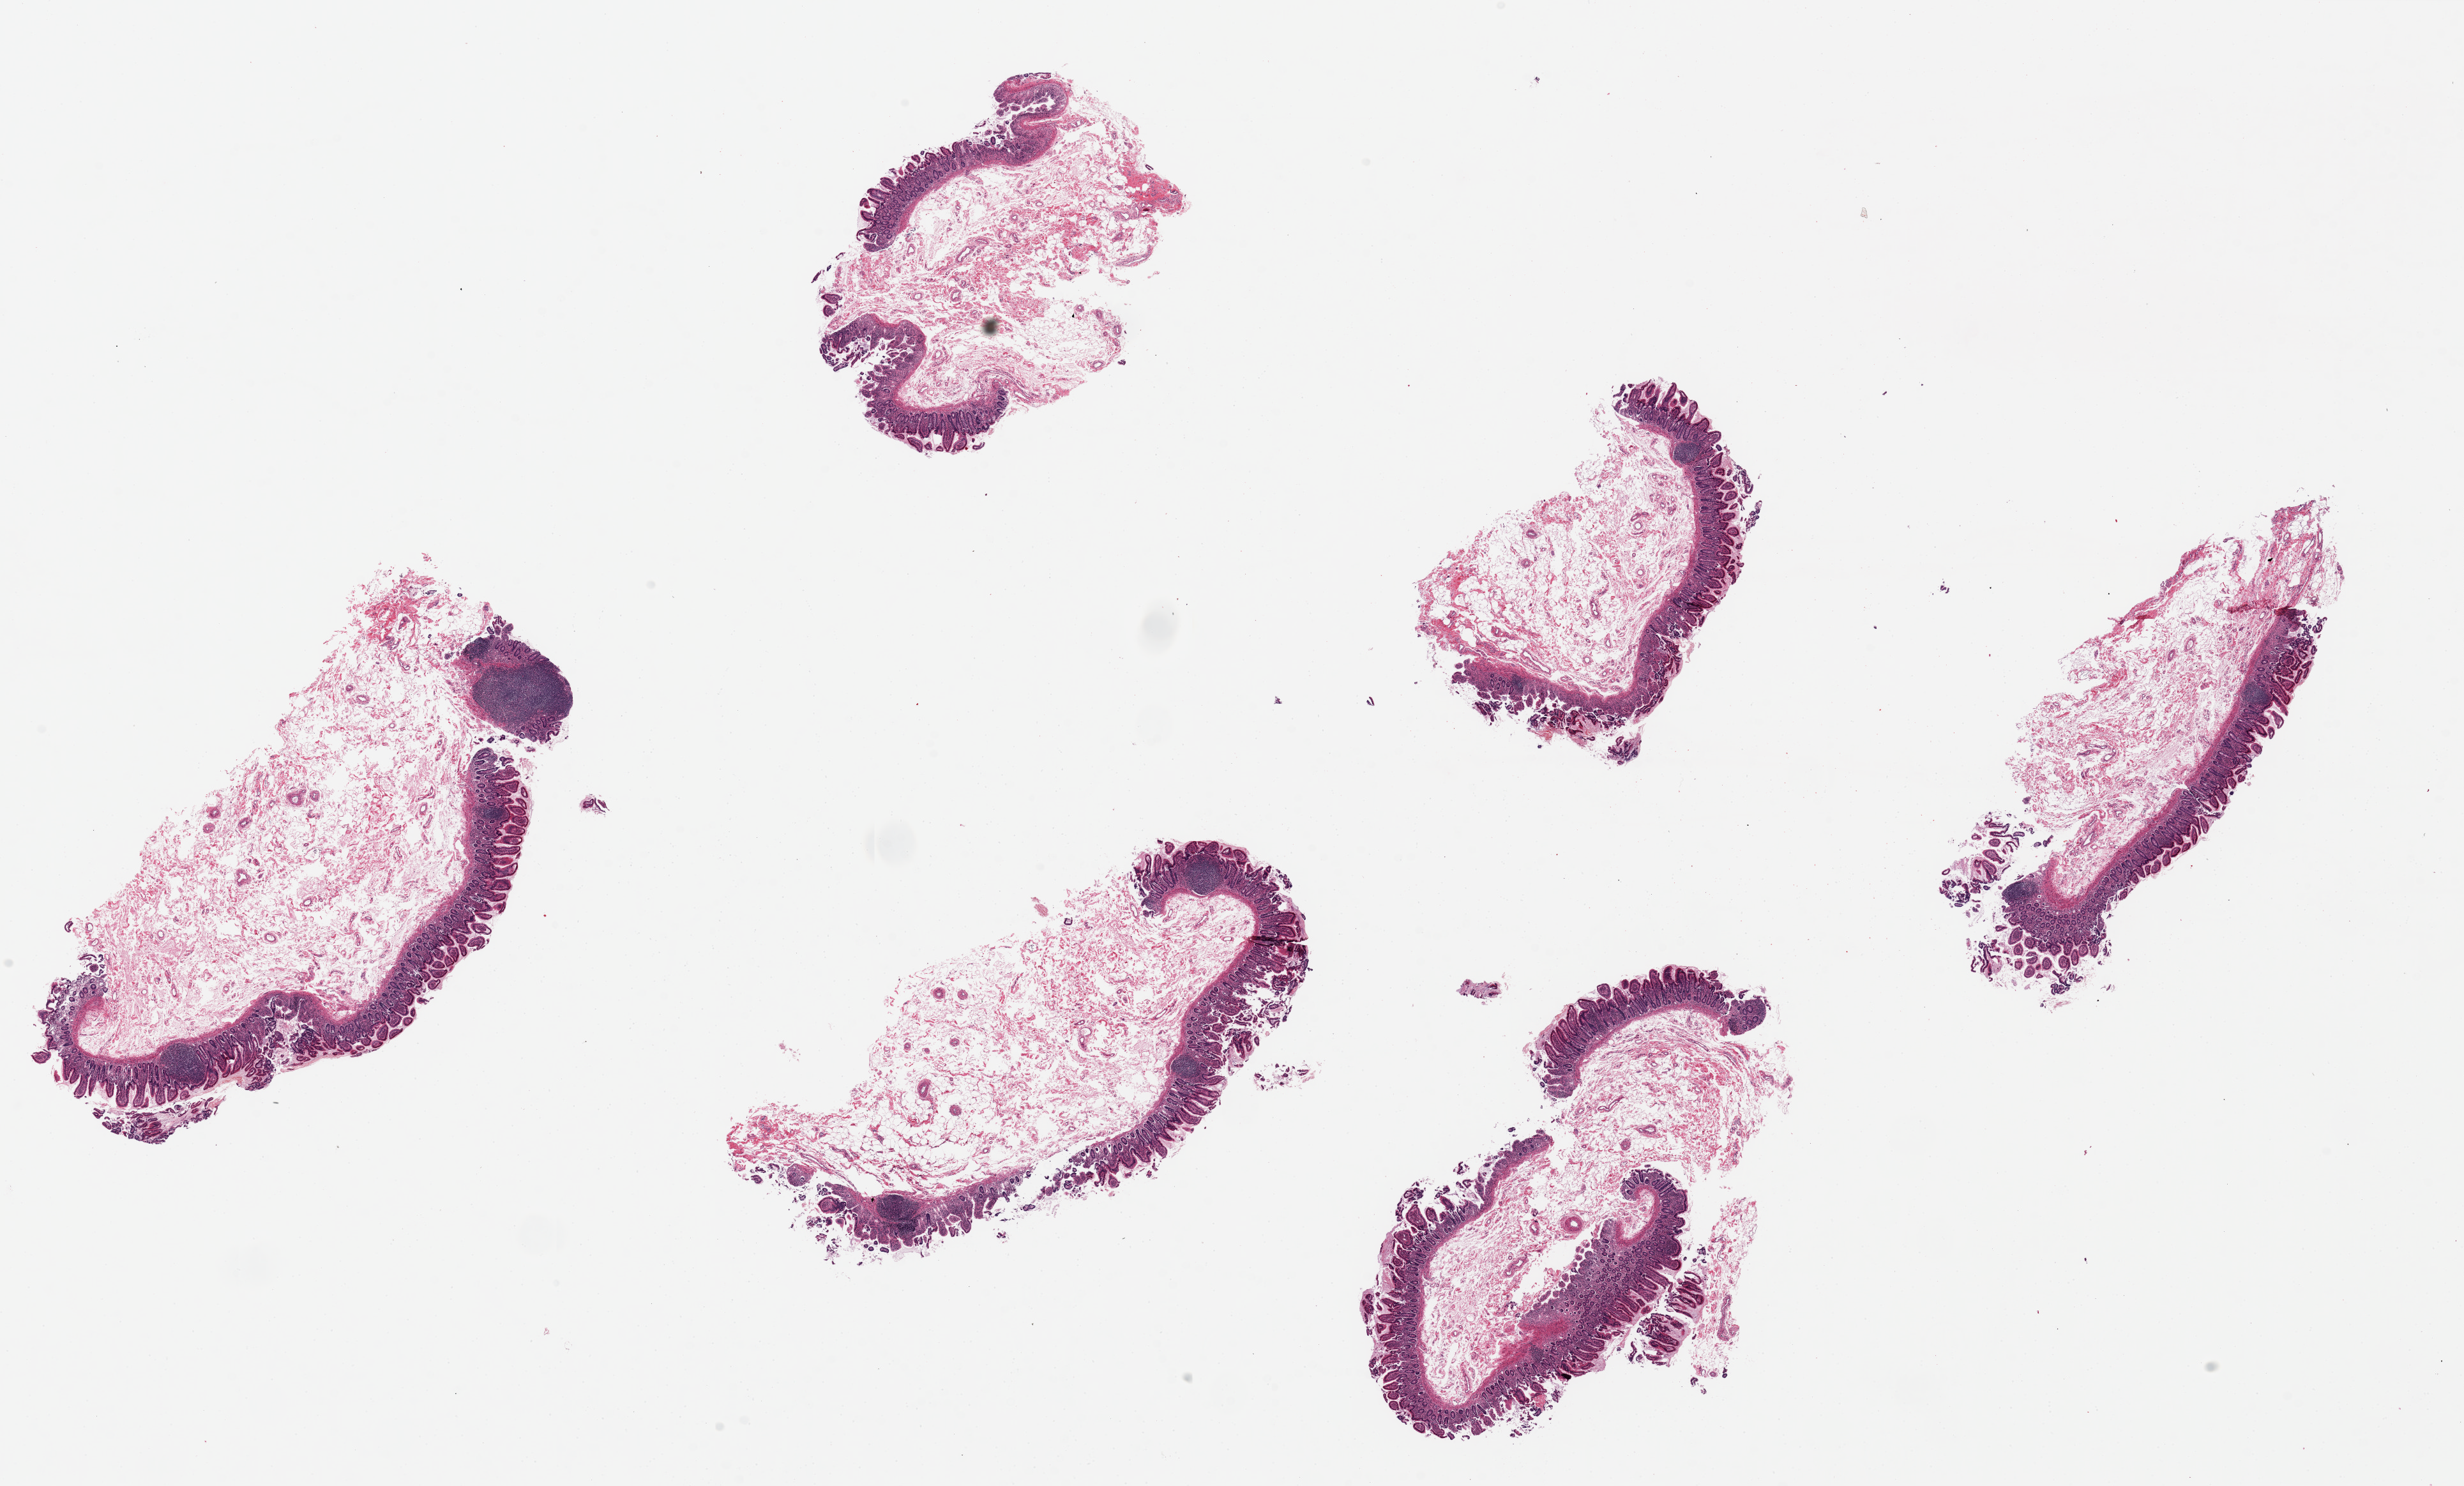
Digitized haematoxylin and eosin-stained section — shown as a low-resolution overview of the whole scanned area (about 30.5 x 18.4 mm), PAXgene-fixed, paraffin-embedded tissue, target tissue: ileum, tissue donor sample. Male donor.
Pathologist's review note for this sample: 6 ~7x3mm pieces; mainly mucosa, rare lymphoid aggregates present.